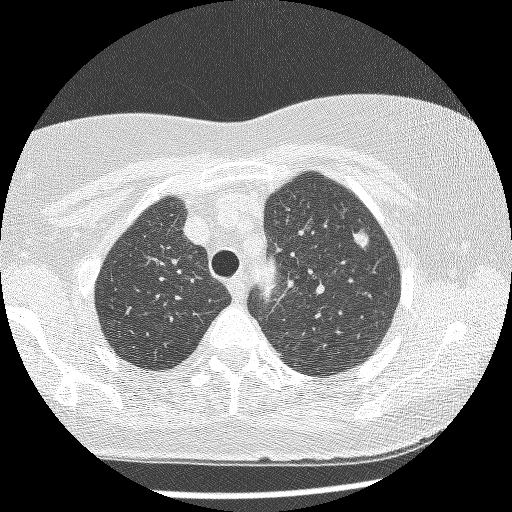
Low-dose screening chest CT, axial slice. Baseline annual screen. Lung window (W 1500 / L -600 HU). 1.25 mm slice thickness. Lung (sharp) reconstruction kernel (BONE). Slice 185 of 241 in the series. 512 × 512 image matrix, field of view 305 × 305 mm. Female participant, aged 61 years at enrolment. Current smoker at enrolment.
• Expert-annotated lung lesion, box from (x=330, y=220) to (x=384, y=269) px.
• The screening reader recorded 4 non-calcified nodules or masses ≥4 mm on this exam (right lower lobe, right middle lobe, right lower lobe, left upper lobe); which of them this box marks is not recorded.
• Later outcome: lung cancer diagnosed 111 days after this screen — bronchiolo-alveolar adenocarcinoma, NOS, left upper lobe, stage IV (AJCC 6th edition), 10 mm at pathology.